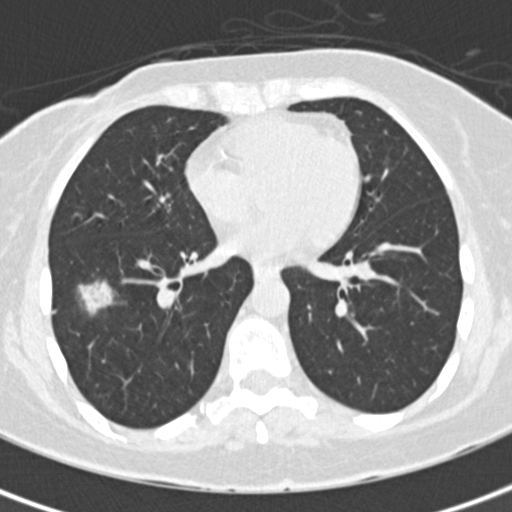
Low-dose screening chest CT, one axial slice; slice 75 of 171 in the series (ordered by position); reconstruction kernel B30f; lung window (W 1500 / L -600 HU); 2 mm slice thickness; 512 × 512 image matrix, field of view 284 × 284 mm.
Outlined on this slice (manually delineated by an expert):
- lesion 1 (tumor, lower lobe of right lung): bounding box <78,281,114,315> (left, top, right, bottom; pixels)